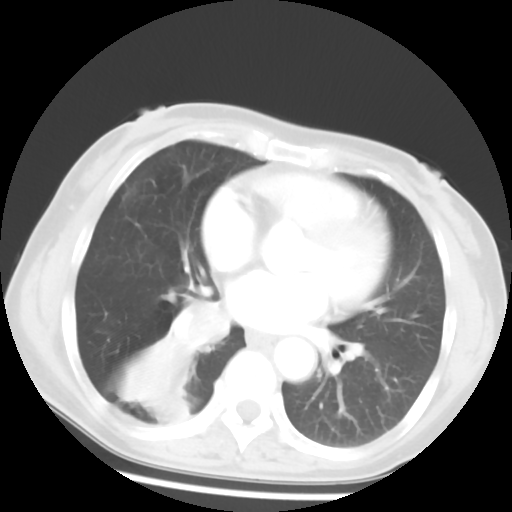
Chest CT, one axial slice. Slice 25 of 52 in the series (ordered by position). 120 kVp. Lung window (W 1500 / L -600 HU). 5 mm slice thickness. 512 × 512 image matrix, field of view 297 × 297 mm. Female patient, age 54 years. Case-level facts recorded for this patient, not image findings: clinical TNM (as recorded): T1c N0 M0.
Annotated regions visible in this slice (bounding box drawn by a radiologist):
- lung tumour (recorded histology: squamous cell carcinoma): bounding box [x1, y1, x2, y2] px = [169, 295, 232, 358]